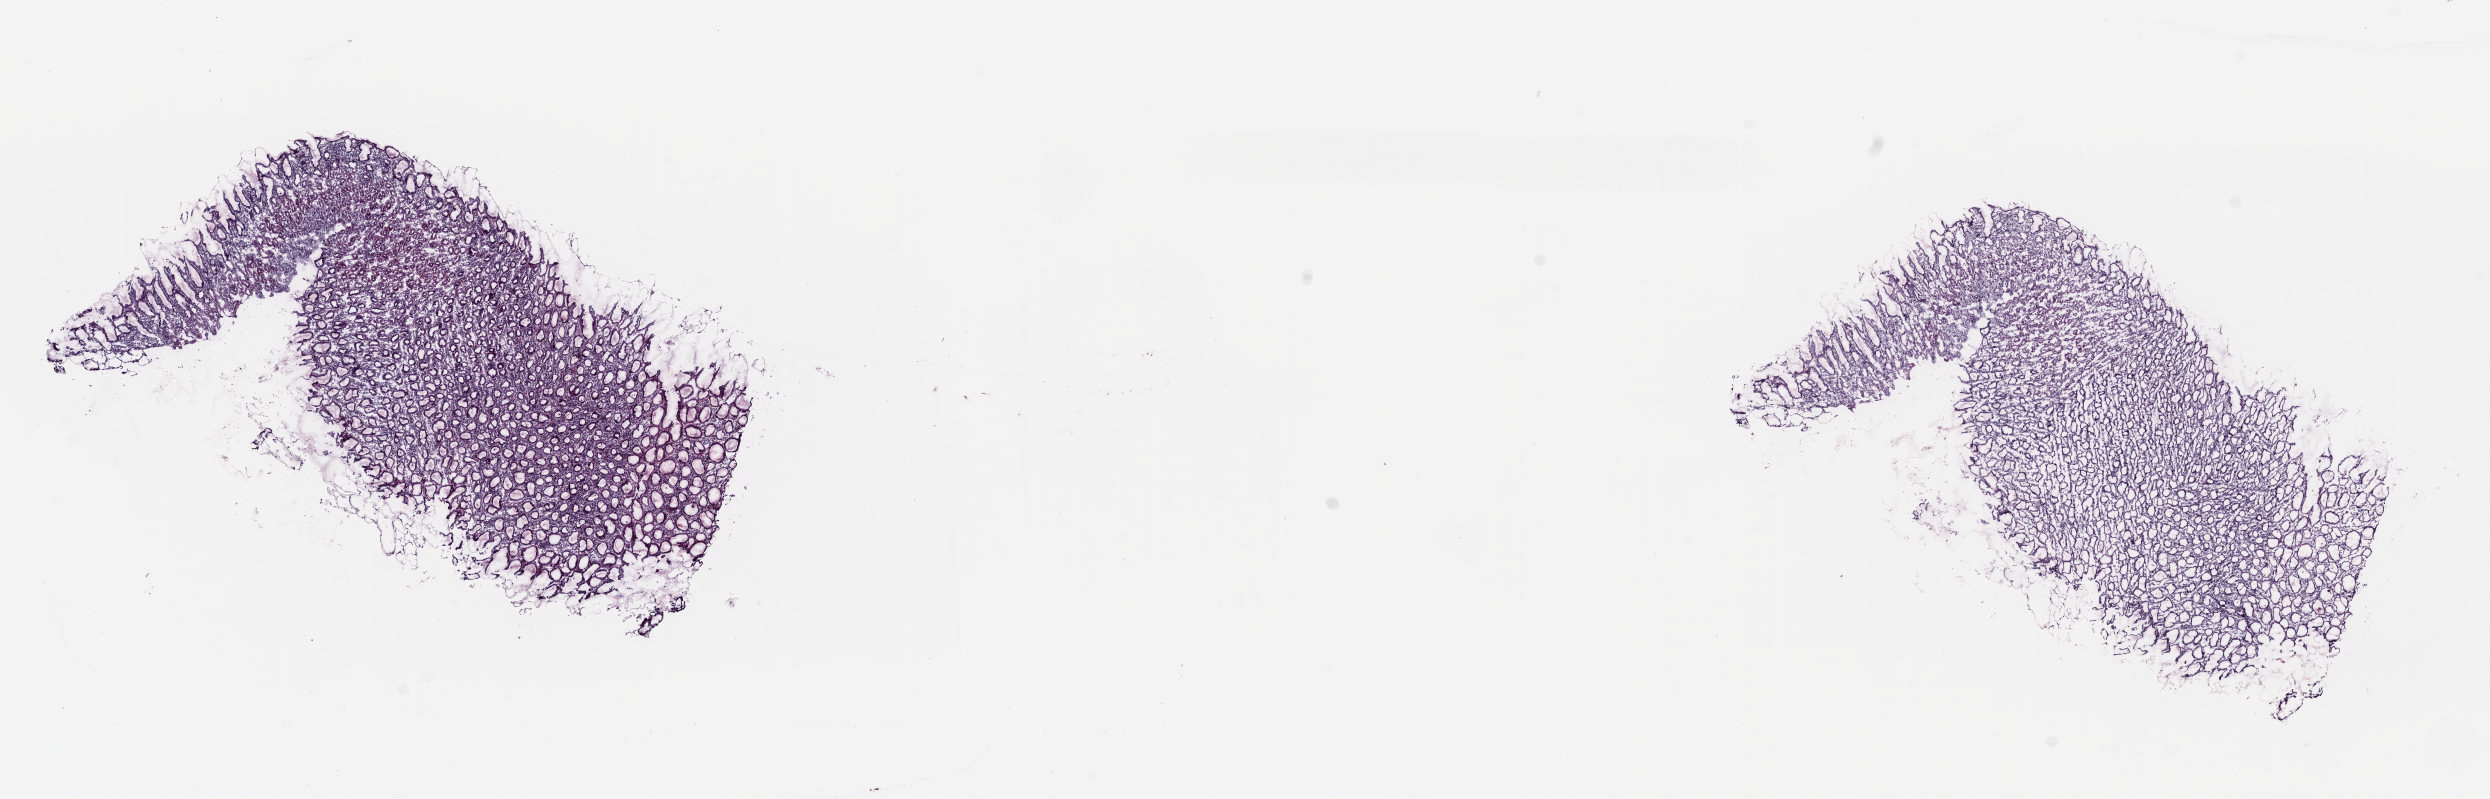
H&E-stained whole-slide image, low-resolution overview of the scanned area, about 19.7 x 6.3 mm (slide scanned at 20x). Frozen section from the top of the tissue portion. Solid tissue normal (non-tumour tissue) sample from the esophagus. Patient: female, age at initial diagnosis 84 years. Slide review estimates, as recorded: tumour cells 0%, tumour nuclei 0%, normal cells 100%, stromal cells 0%, necrosis 0%. Infiltration values recorded for this section: lymphocyte infiltration 10%, monocyte infiltration 0%, neutrophil infiltration 0%.
* this section: solid tissue normal (non-tumour) sample from the same patient
* patient diagnosis: Adenocarcinoma, NOS (lower third of esophagus)